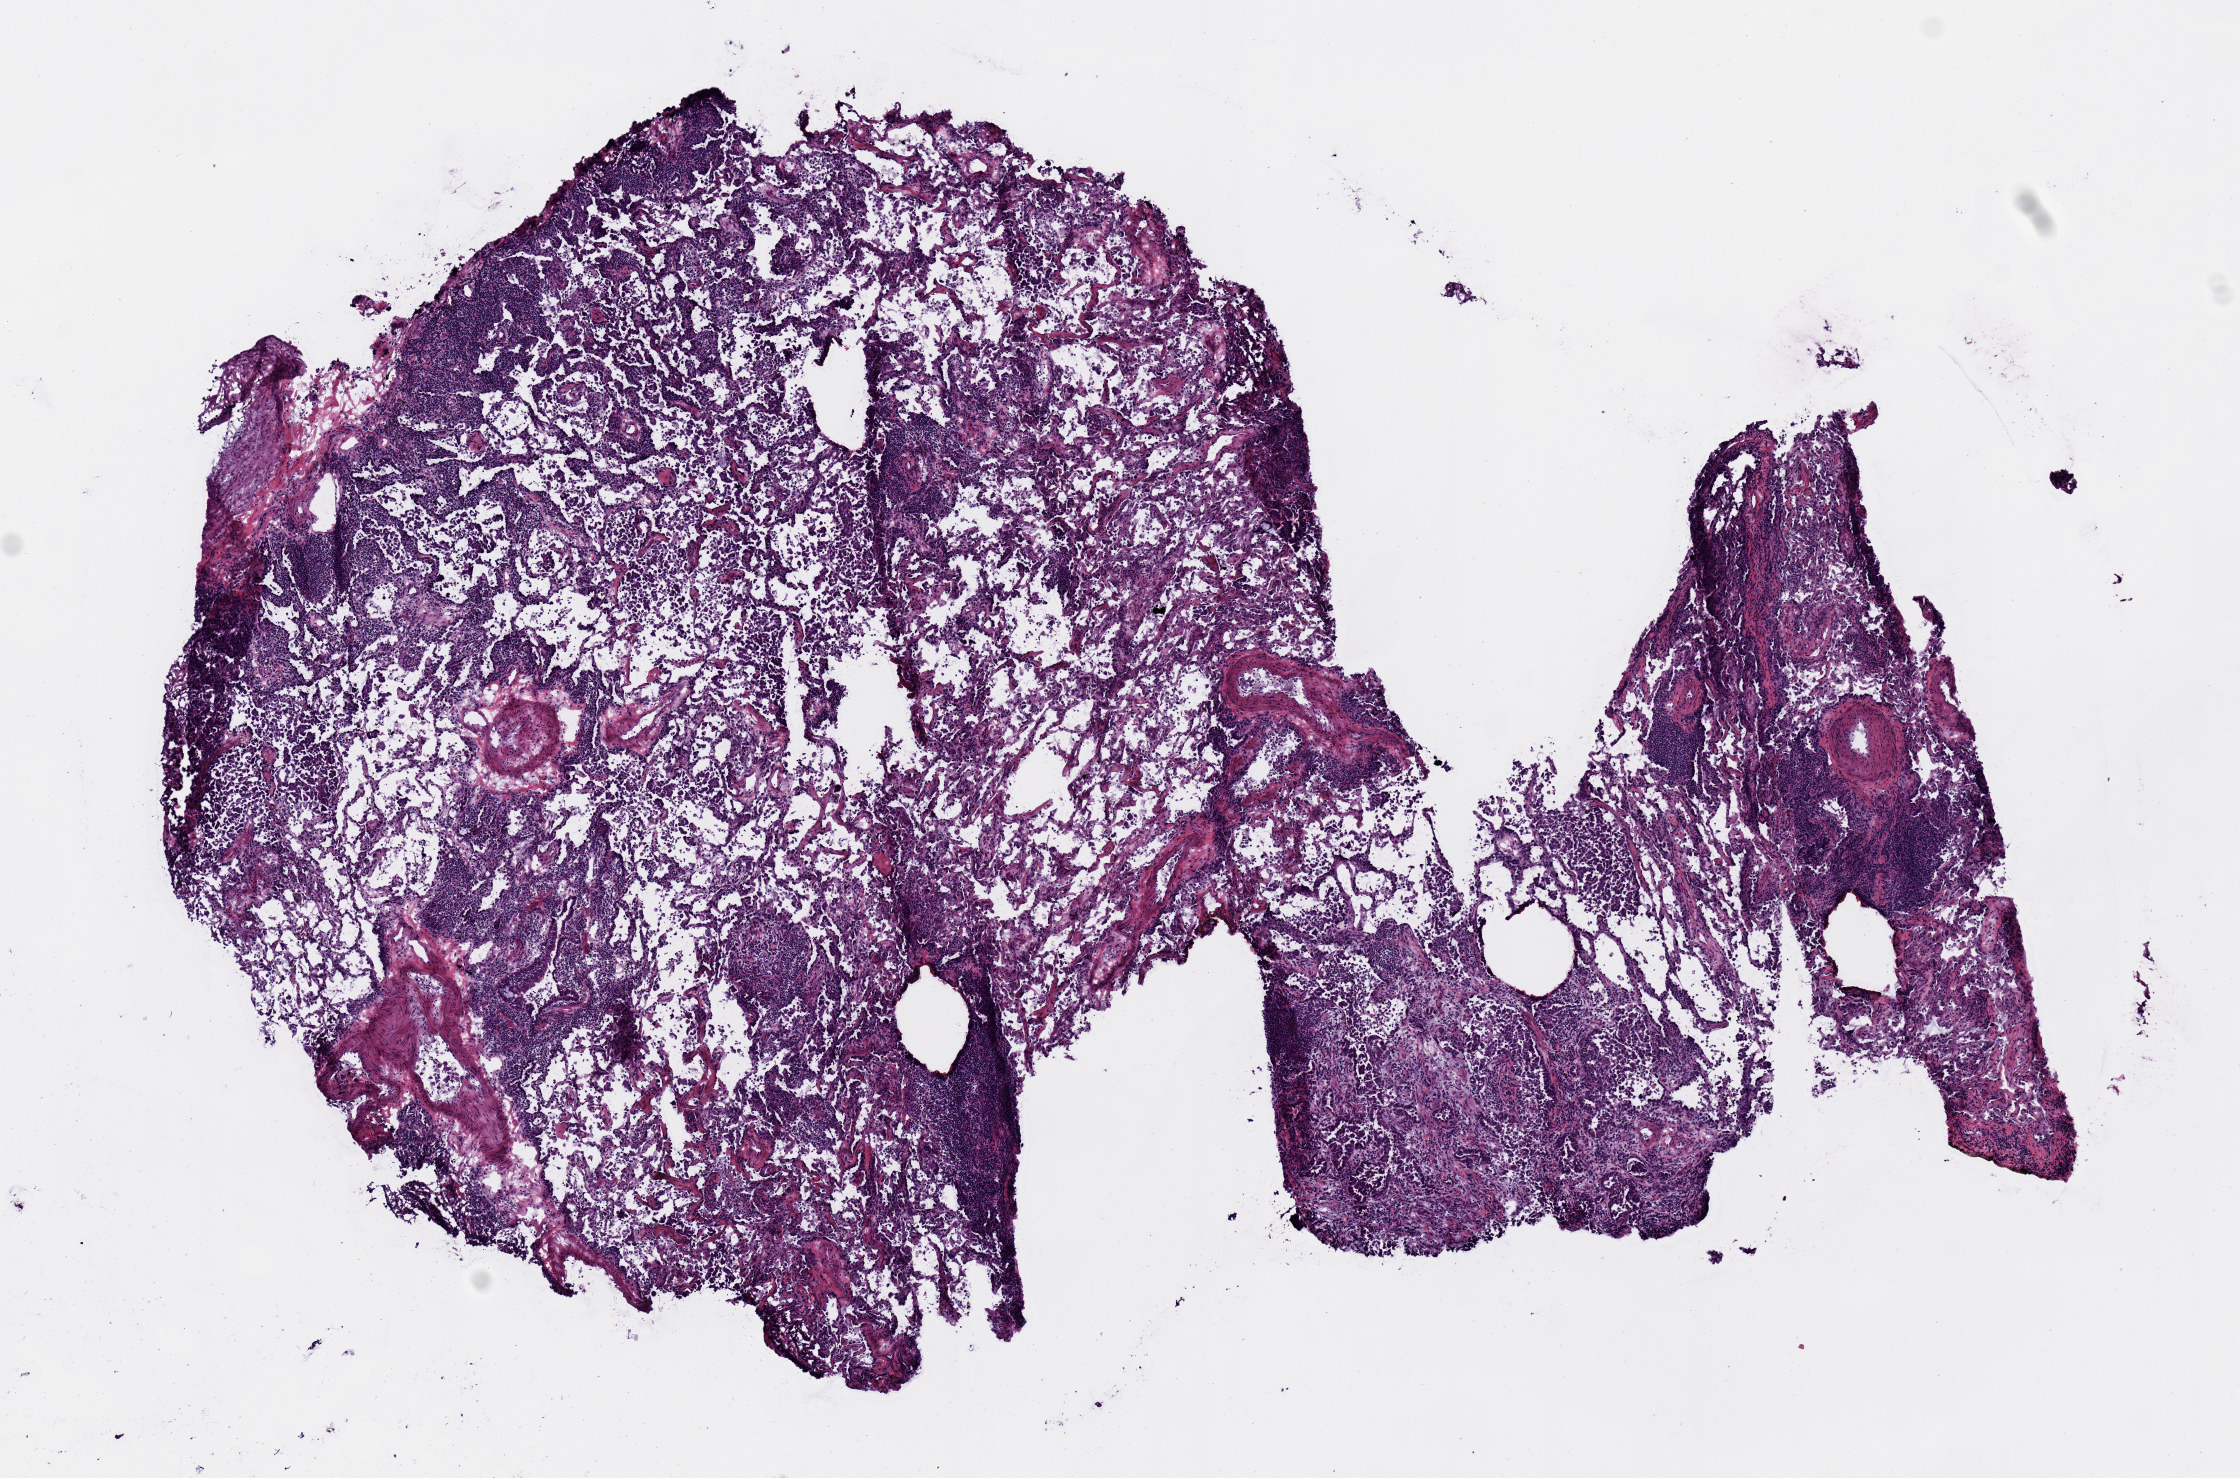
H&E-stained whole-slide image — whole scanned area (about 8.9 x 5.8 mm) shown as a low-resolution overview; frozen section; lung, primary tumour sample. Patient: female, age at initial diagnosis 71 years. Pathologist review of this section (percent, as recorded): tumour cells 90%, tumour nuclei 60%, normal cells 0%, stromal cells 10%, necrosis 0%.
Diagnosis: Adenocarcinoma, NOS (upper lobe, lung). AJCC pathologic stage: IIA (7th edition).